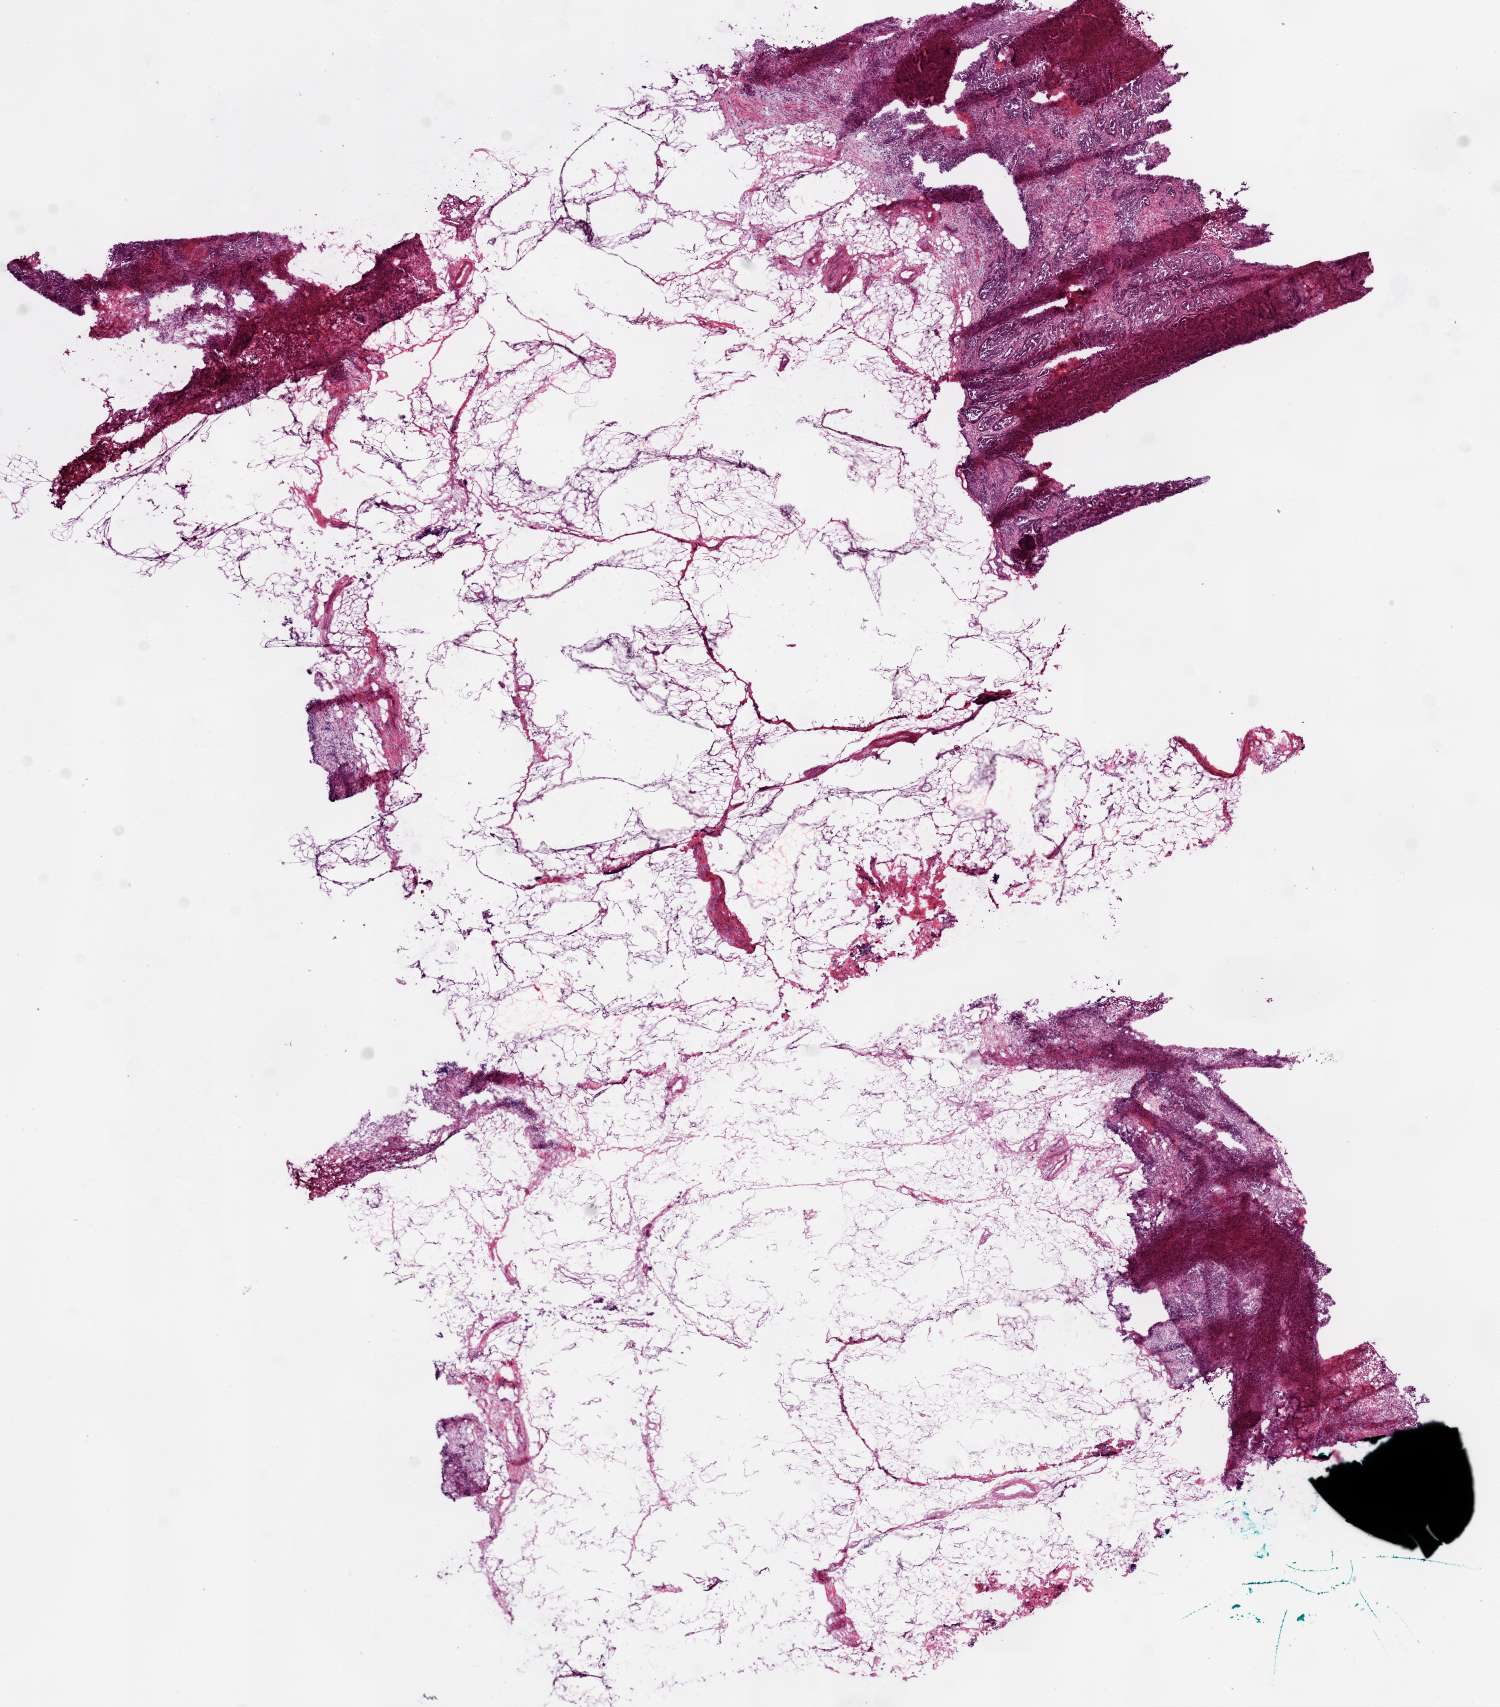
Whole-slide histology image, H&E — a low-resolution overview of the entire scanned area, about 12.0 x 13.7 mm. Frozen section. Primary tumour sample from the ovary. Patient: female, age at initial diagnosis 45 years. Histologic grade: G3 (poorly differentiated). Pathologist review of this section (percent, as recorded): tumour cells 65%, tumour nuclei 75%, normal cells 0%, stromal cells 25%, necrosis 10%.
• FIGO stage: IIIC
• pathologic diagnosis: Serous cystadenocarcinoma, NOS